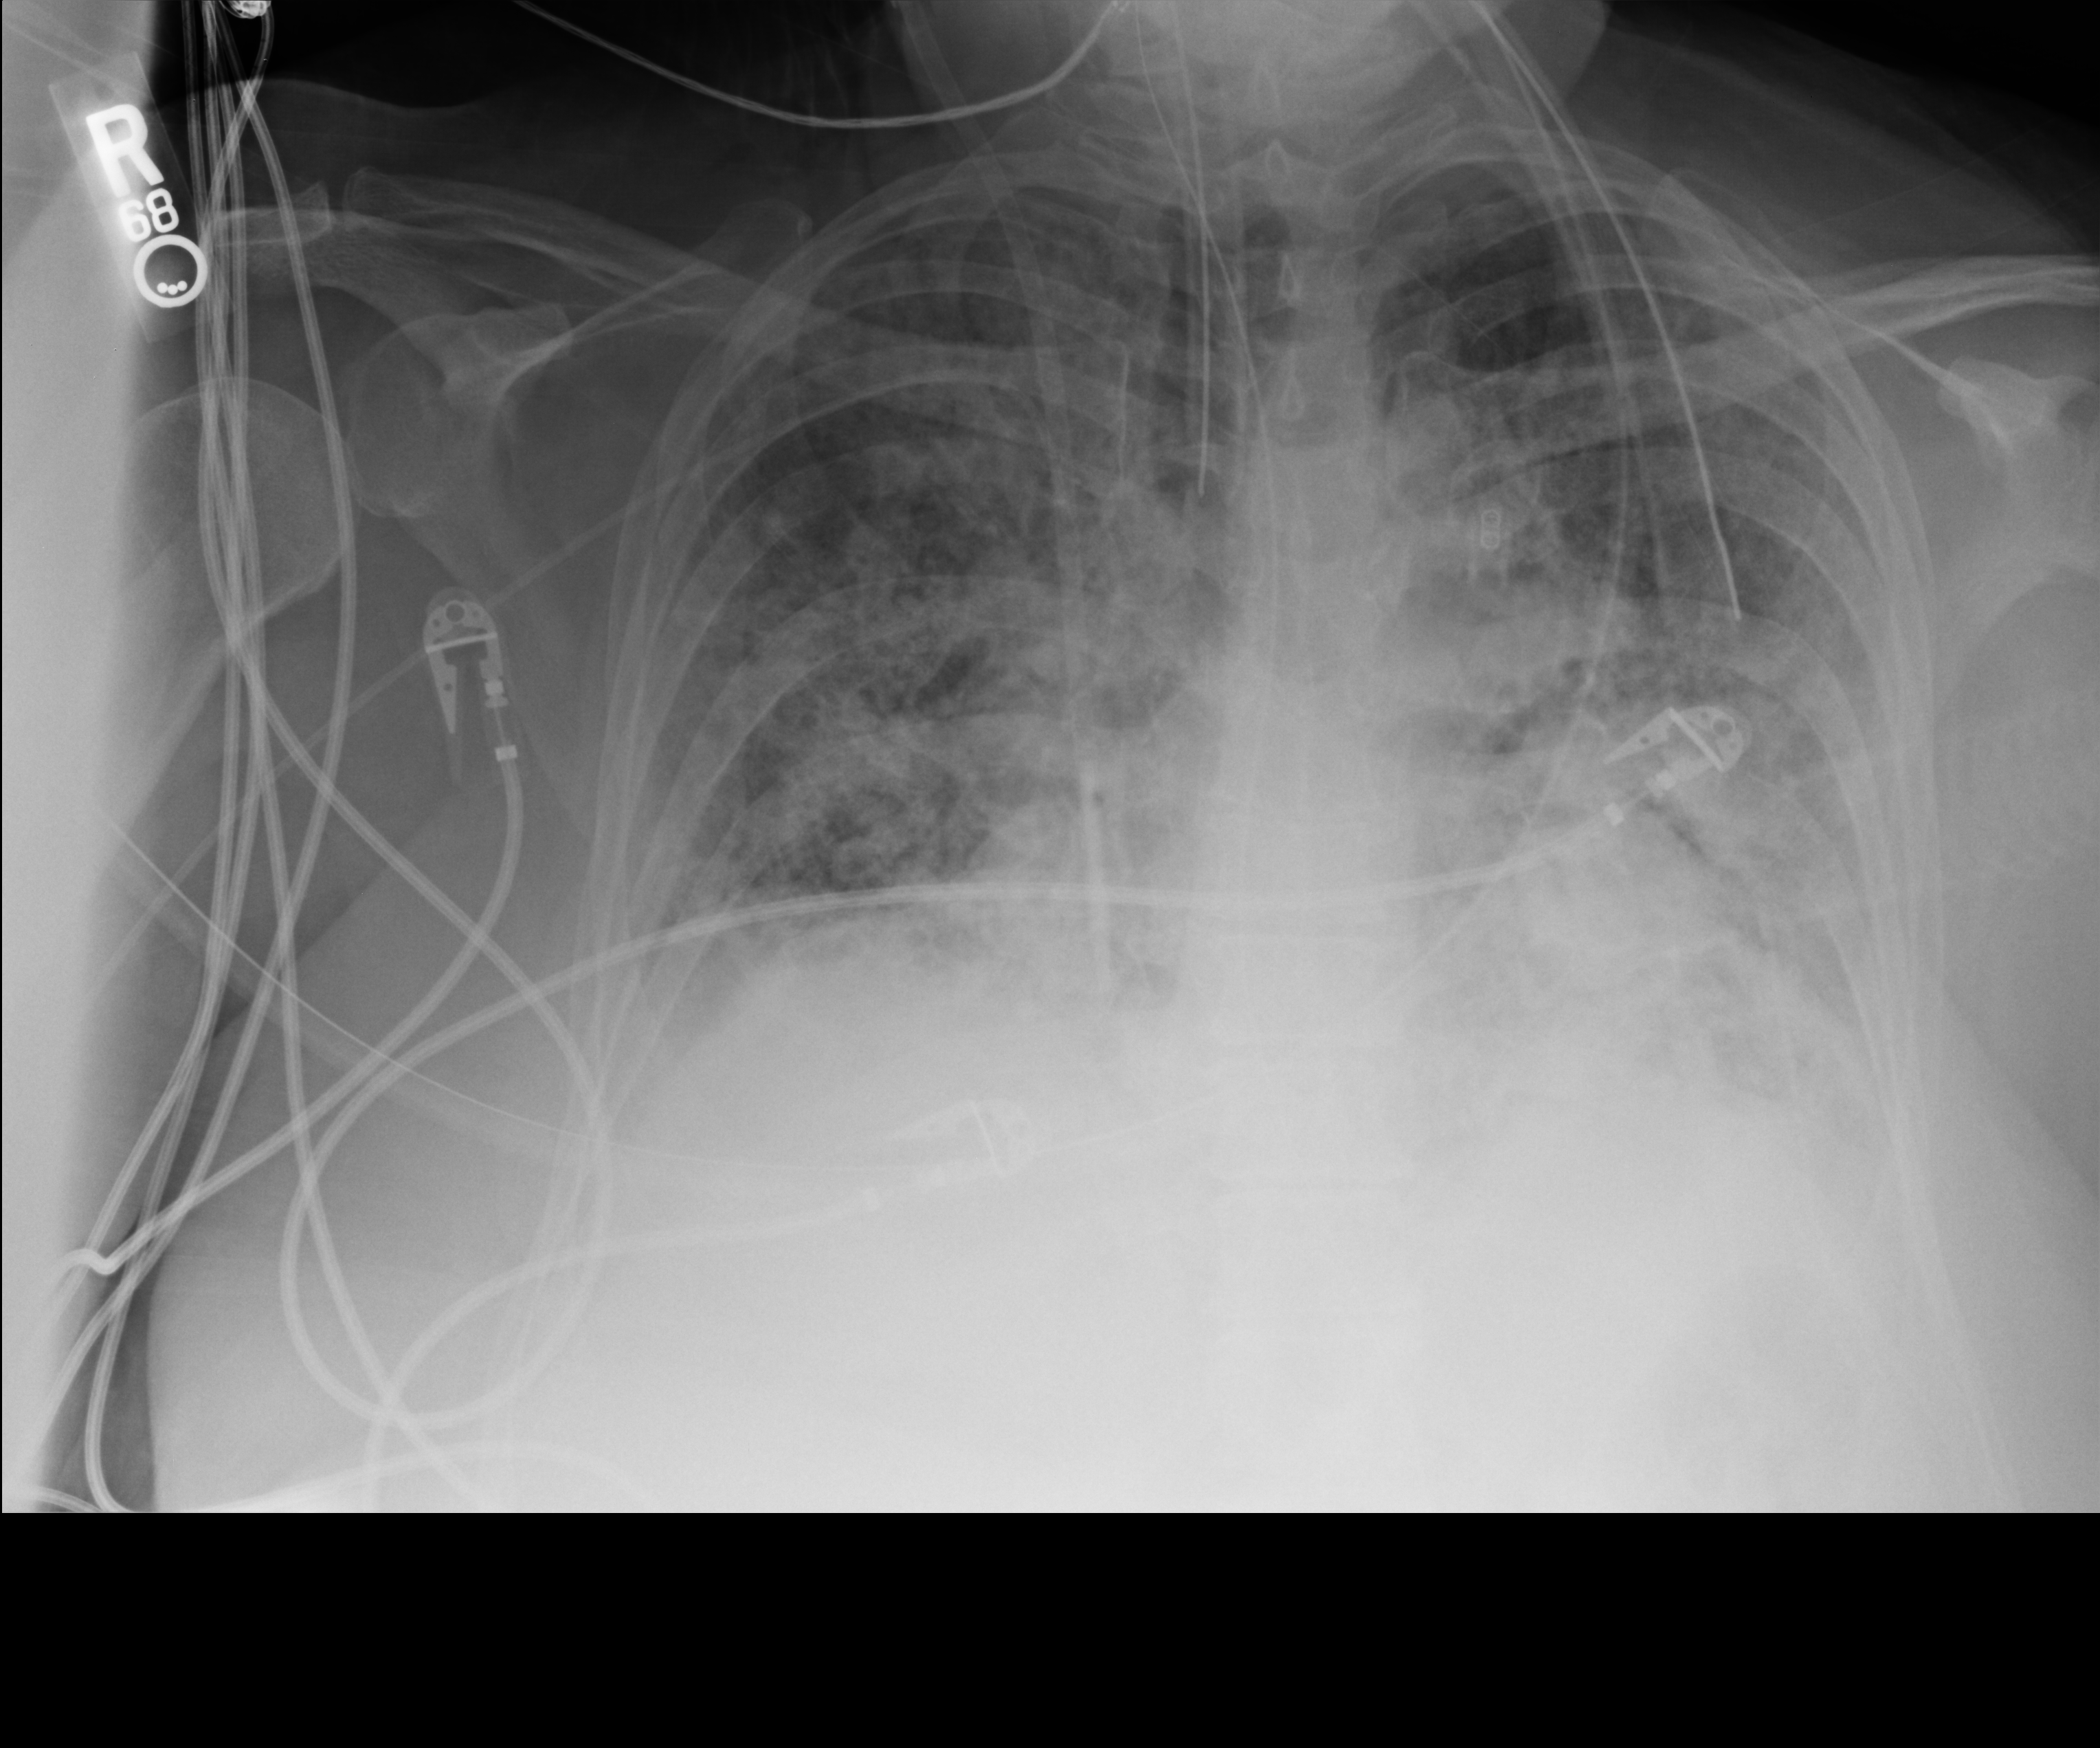
Chest X-ray (portable); anteroposterior (AP) projection. Female patient hospitalised with COVID-19, age 60–74 years.
Hospital-stay facts (about this admission, not read from this image; timing relative to this image not recorded): mechanically ventilated during this hospital stay: yes; admitted to intensive care during this hospital stay: yes.